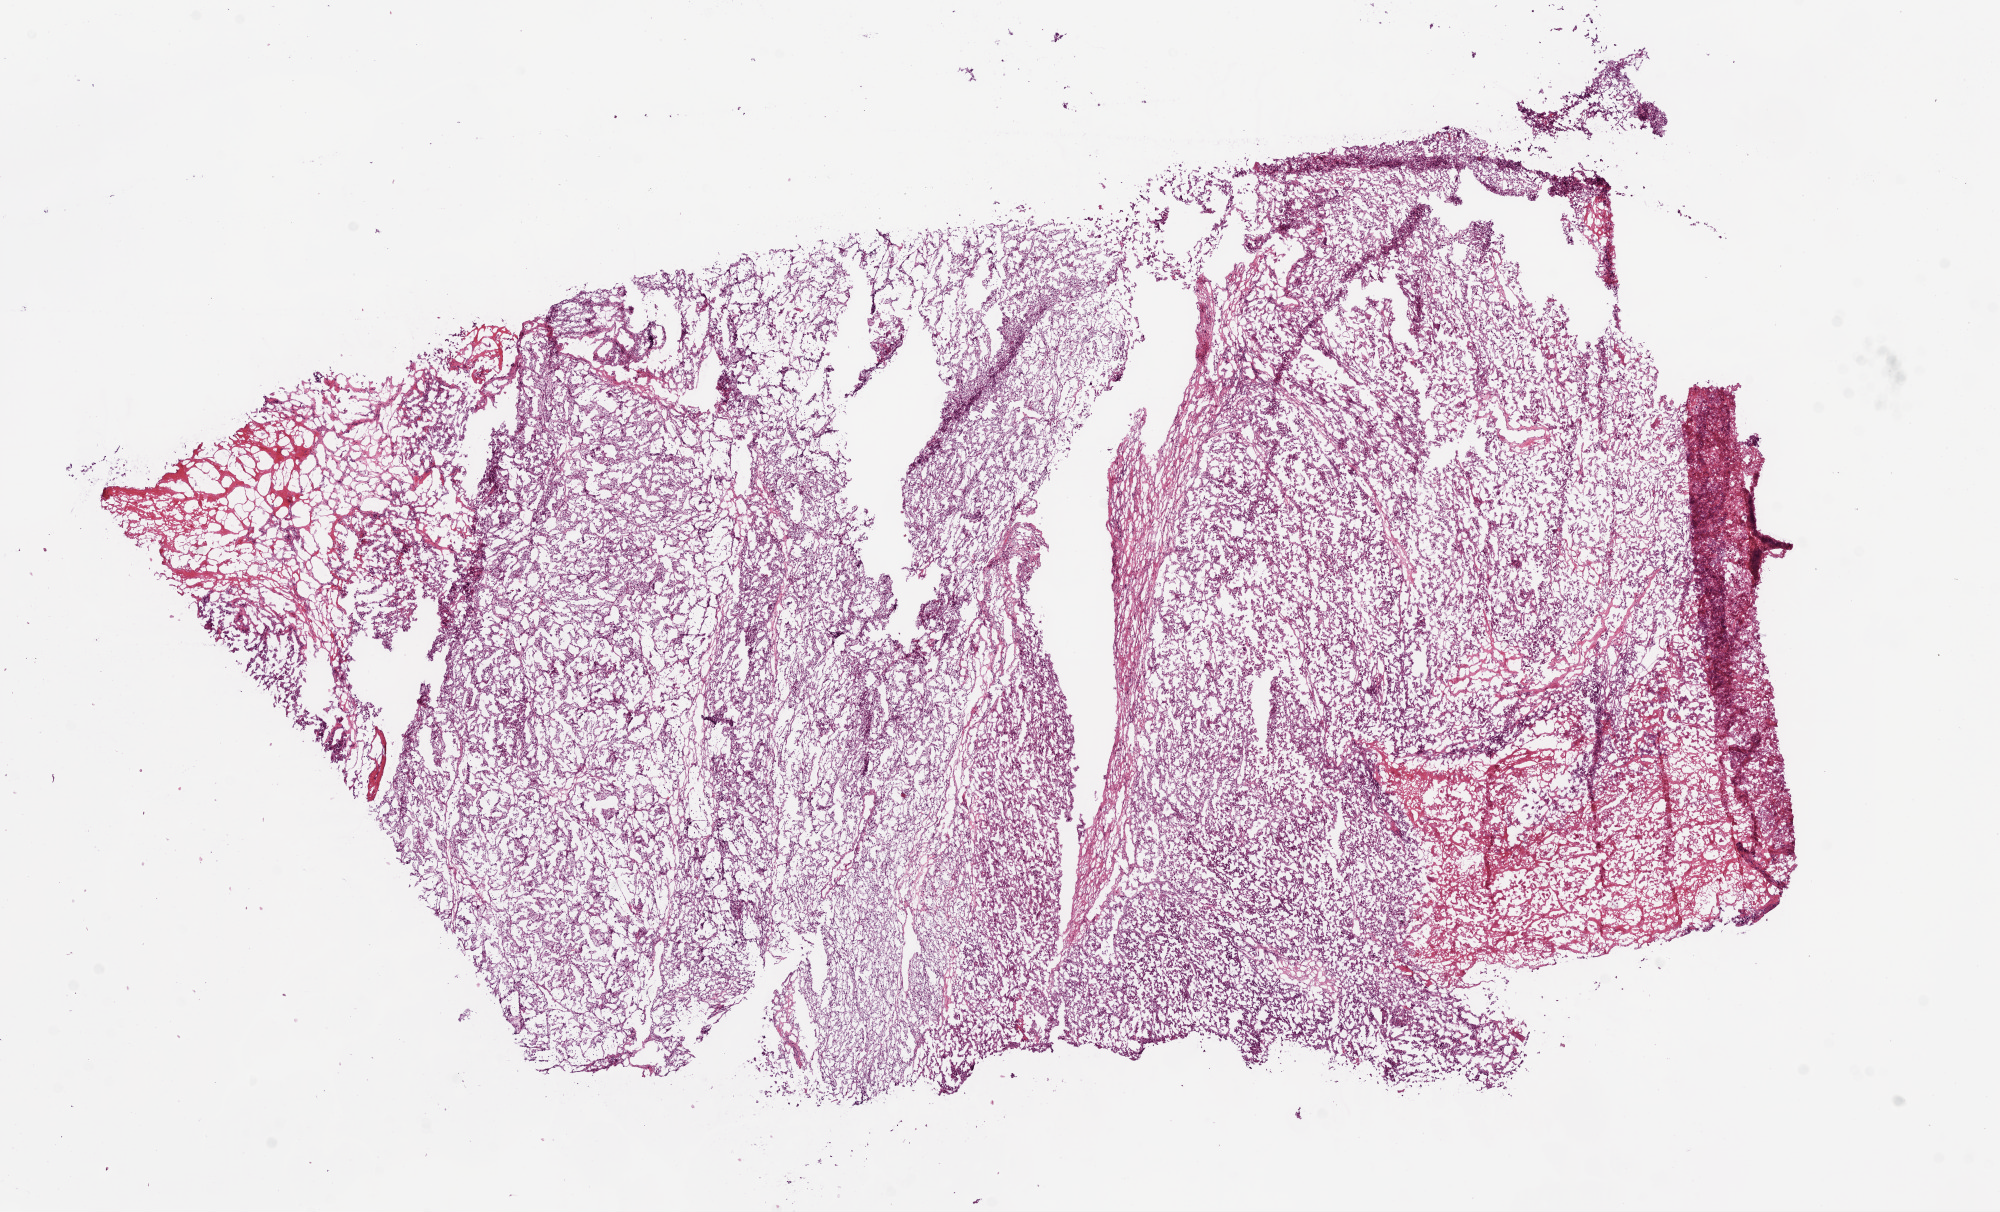
Whole-slide histology image, H&E-stained — shown as a low-resolution overview of the whole scanned area (about 16.0 x 9.7 mm, acquisition: 20x scan). Frozen section. Kidney, primary tumour sample. Female patient; age at initial diagnosis 45 years. Histologic grade: G4 (undifferentiated). Slide review estimates, as recorded: tumour cells 70%, tumour nuclei 85%, normal cells 0%, stromal cells 15%, necrosis 15%.
TNM: T3a NX M0. Diagnosis: Clear cell adenocarcinoma, NOS. AJCC pathologic stage: III.